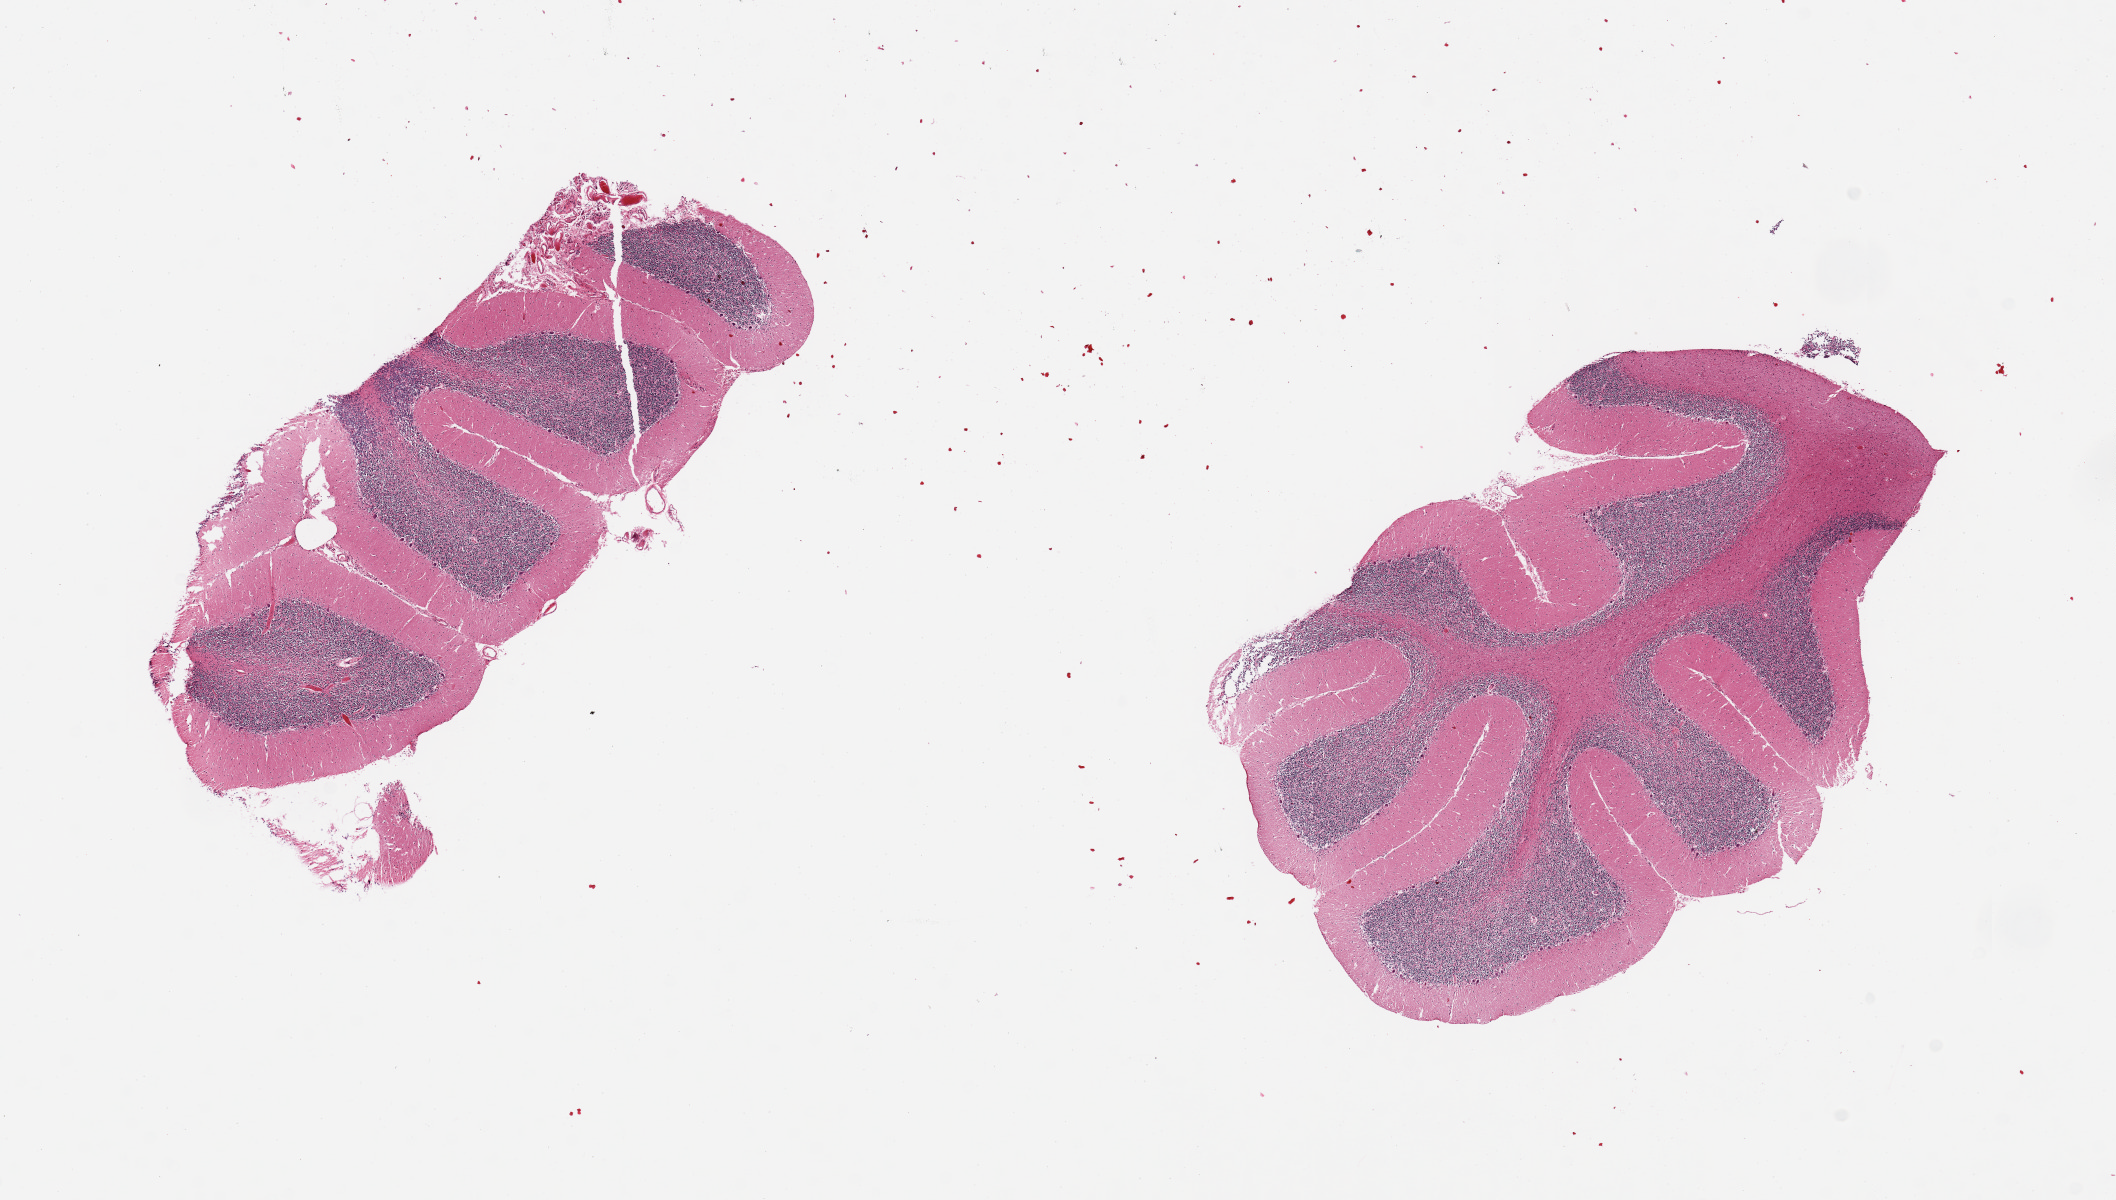
Whole-slide image, H&E stain, brightfield — shown as a low-resolution overview of the whole scanned area (about 16.7 x 9.5 mm, slide scanned at 20x). PAXgene-fixed paraffin-embedded (PFPE) section. Section of cerebellum (target tissue). Tissue donor sample. Donor: male.
Reviewer comment on this tissue sample: 2 pieces.